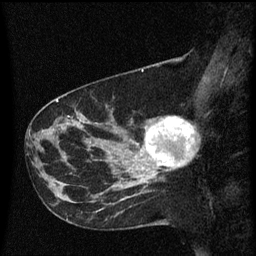
Breast MRI (dynamic contrast-enhanced), one sagittal slice; position 24 of 60 along the scan axis; dynamic contrast-enhanced series, image 2 of 3 at this slice position (ordered by acquisition); 1.5 T; TE 4.2 ms, TR 8.4 ms; 2 mm slice thickness; 256 × 256 image matrix, field of view 200 × 200 mm. Female patient, age 41 years. Case-level facts recorded for this patient, not image findings: setting: breast cancer imaged before/during neoadjuvant chemotherapy; receptor status: triple-negative.
Annotated regions visible in this slice (semi-automatically segmented with operator editing):
- analysis volume of interest (the breast-tissue region the enhancement analysis was run in; not a lesion): box from (x=138, y=116) to (x=196, y=177) px
- tumour enhancement mask (voxels above the 70 % enhancement threshold inside the analysis volume of interest): (x=146, y=116)–(x=194, y=167)